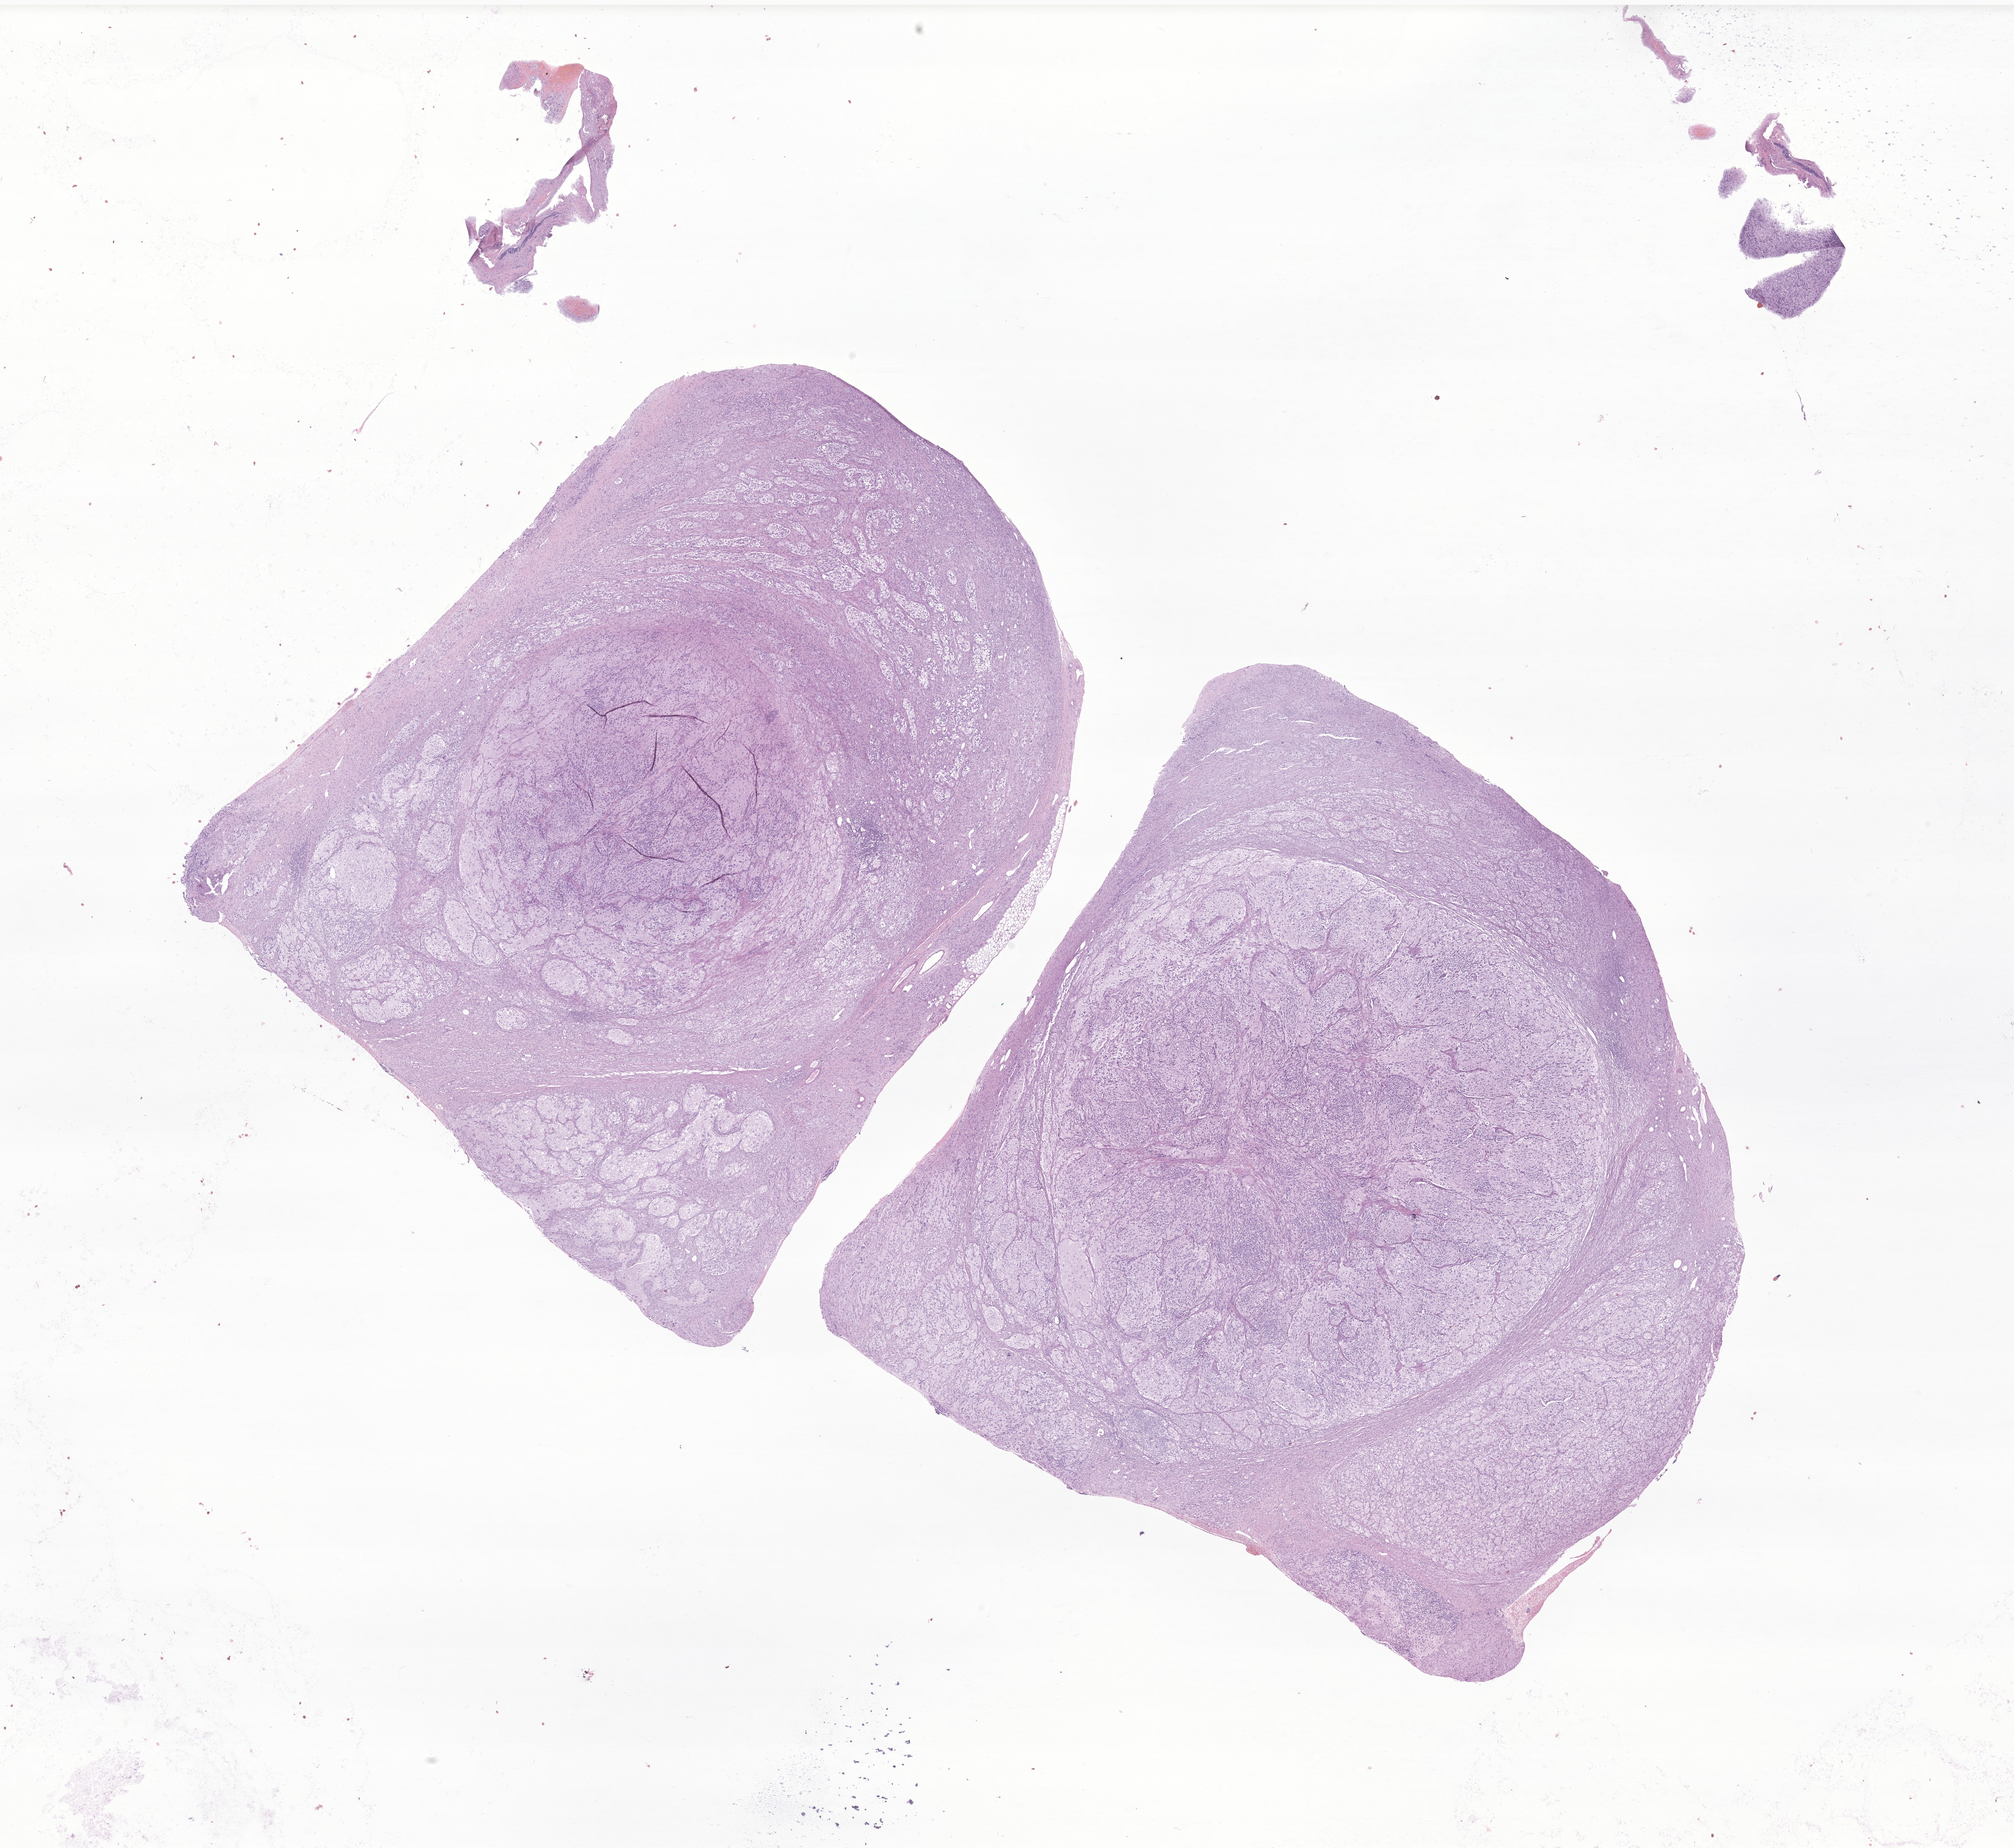
Digitized H&E-stained section of tumor tissue from the adrenal gland, shown as a low-resolution overview of the whole scanned area (about 21.7 x 19.9 mm). Formalin-fixed paraffin-embedded section. Male patient, age 894 days (about 2.4 years).
- recorded diagnosis: Neuroblastoma, NOS